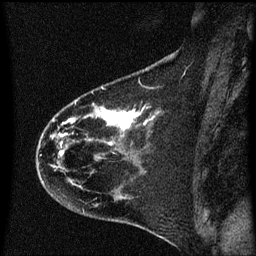
Breast MRI (dynamic contrast-enhanced), one sagittal slice; slice 23 of 60 in the series (ordered by position); dynamic contrast-enhanced series, image 2 of 3 at this slice position (ordered by acquisition); 1.5 T; TE 4.2 ms, TR 8.4 ms; 2 mm slice thickness; 256 × 256 image matrix. Female patient, age 35 years. Case-level facts recorded for this patient, not image findings: setting: breast cancer imaged before/during neoadjuvant chemotherapy; receptor status: HER2-positive.
Outlined on this slice (semi-automatic segmentation, software-assisted and operator-edited):
- analysis volume of interest (the breast-tissue region the enhancement analysis was run in; not a lesion): bounding box <37,68,174,173> (left, top, right, bottom; pixels)
- tumour enhancement mask (voxels above the 70 % enhancement threshold inside the analysis volume of interest): <59,108,154,155>